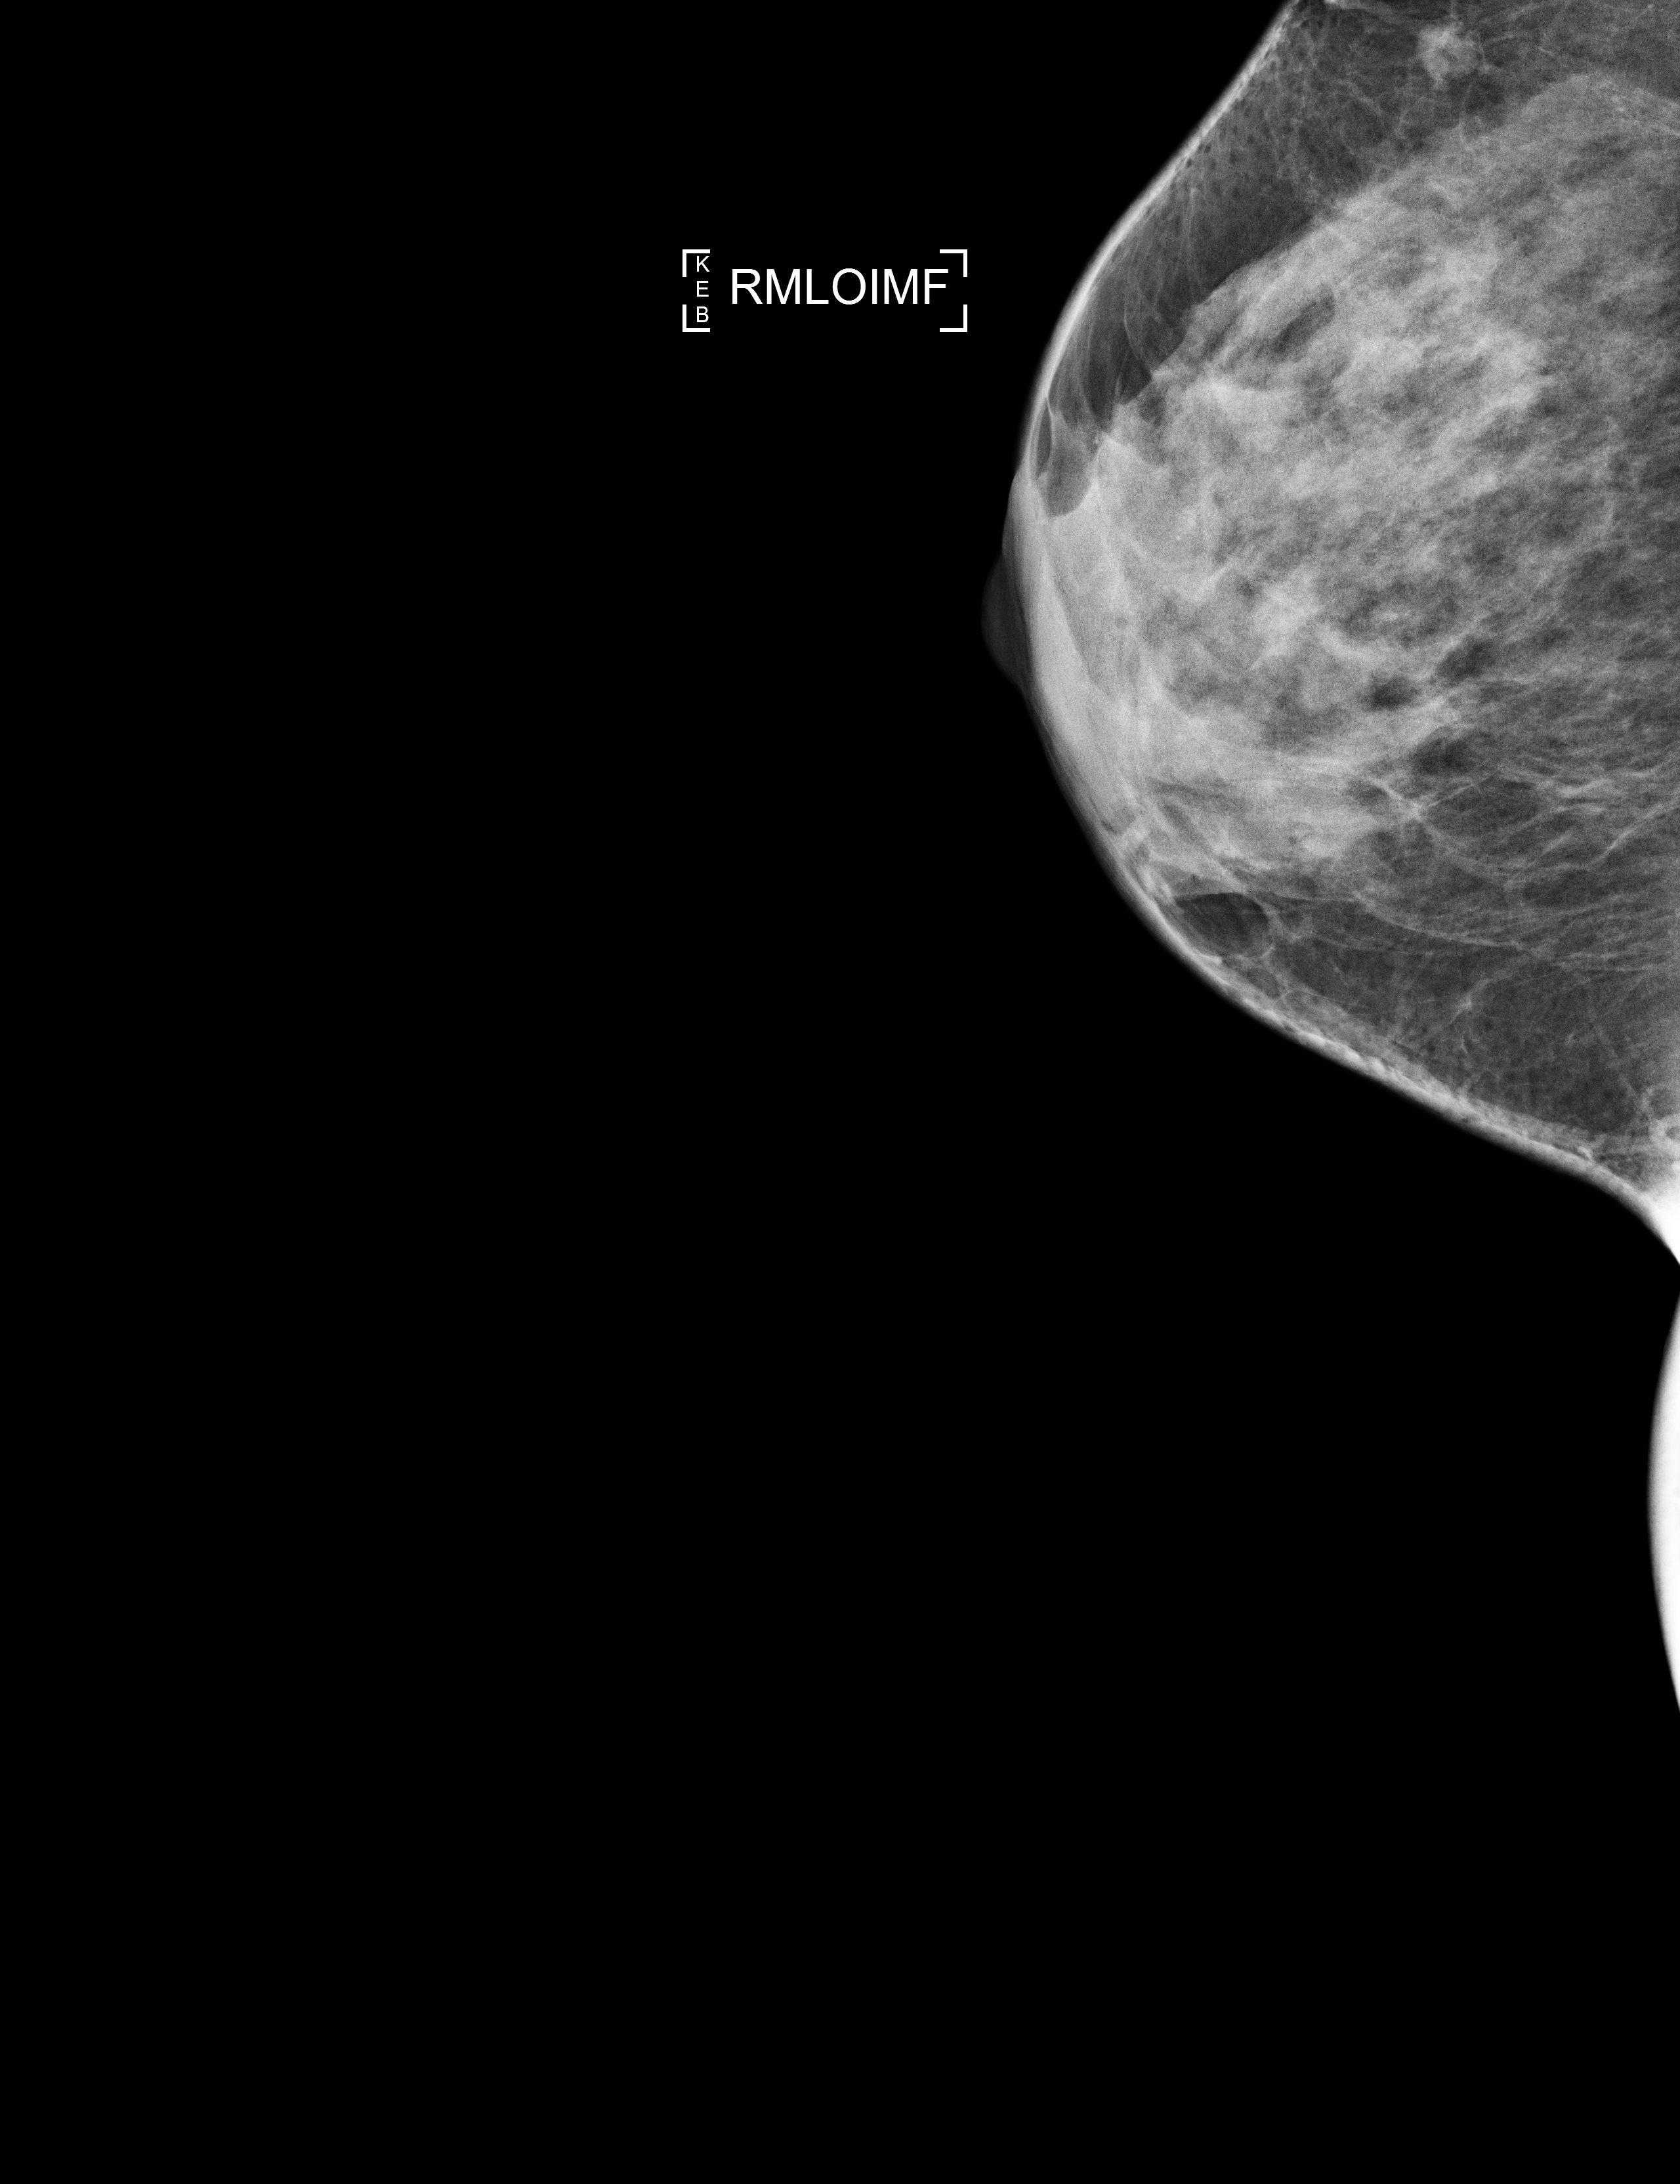
Full-field digital mammogram (FFDM); right breast; mediolateral oblique (MLO) view (infra-mammary fold); annual screening mammography examination. Female patient, age 44 years.
Final BI-RADS assessment for this screening round (tomosynthesis exam, both breasts): category 2.